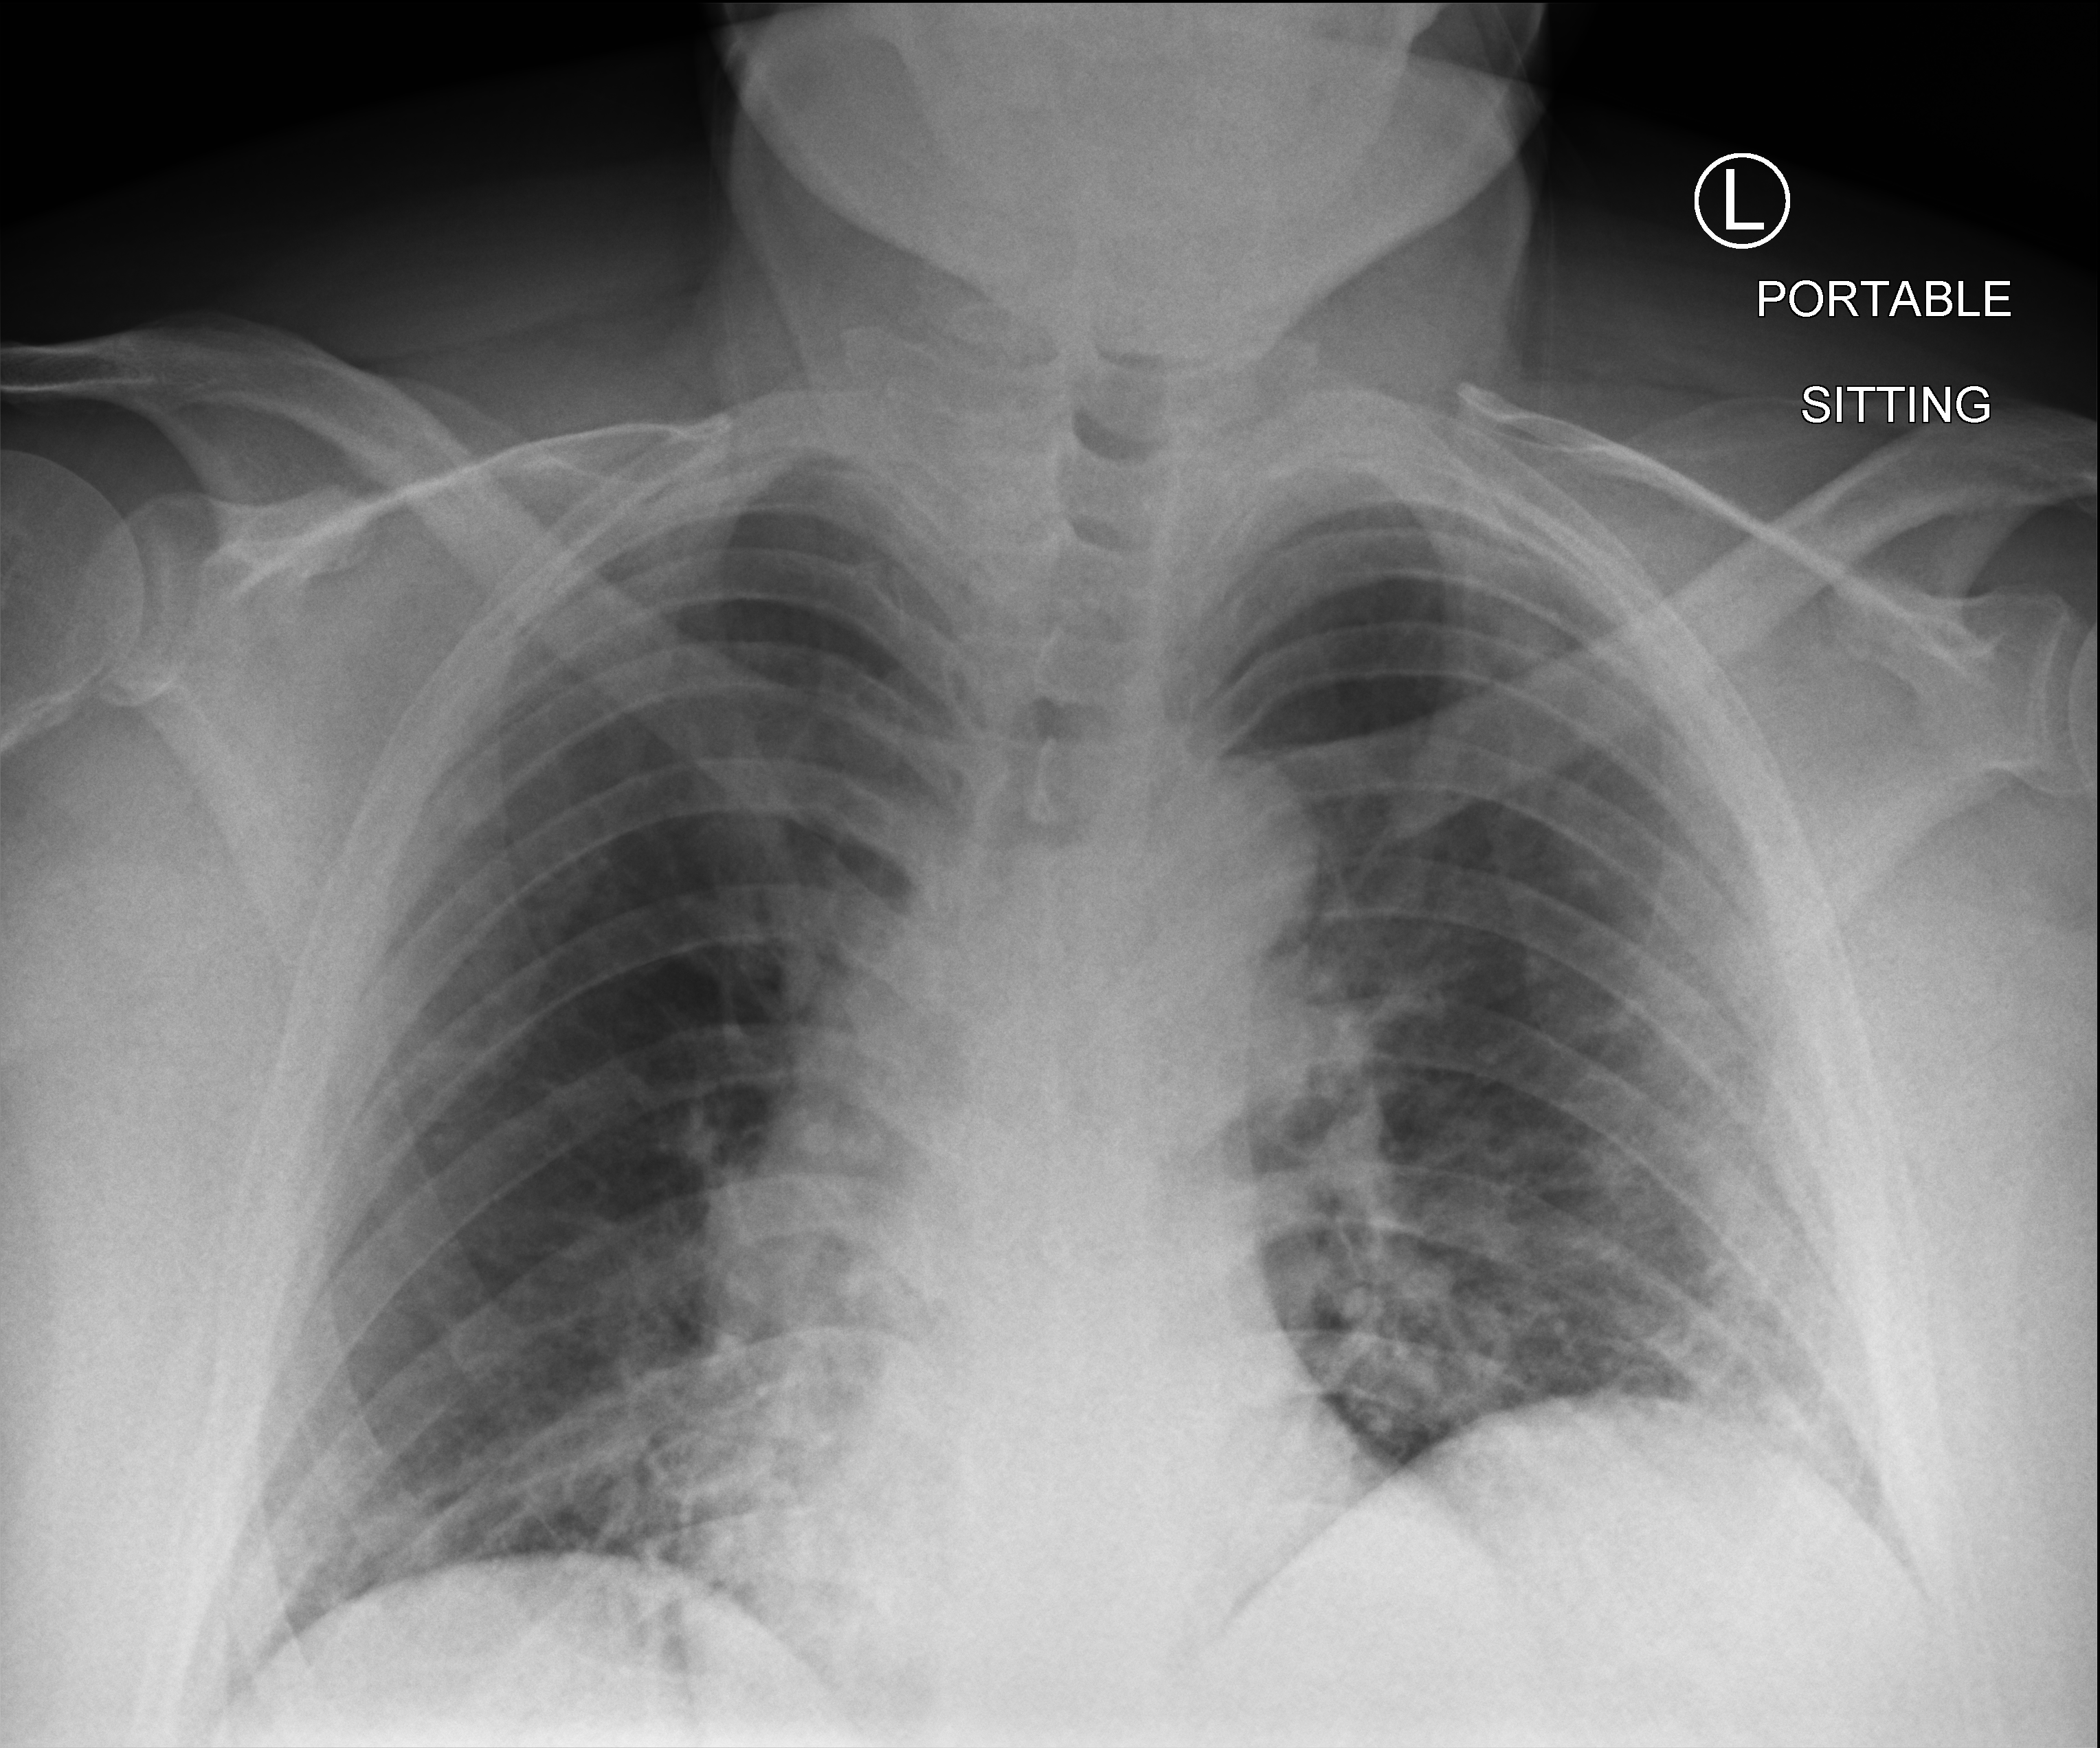
Portable chest radiograph, anteroposterior (AP) projection. Patient hospitalised with COVID-19; male, aged 18–59 years.
Admission-level facts for this patient (not findings on this image; timing relative to this image not recorded): mechanically ventilated during this hospital stay: no; diabetes (admission record): no; length of hospital stay: 6 days.